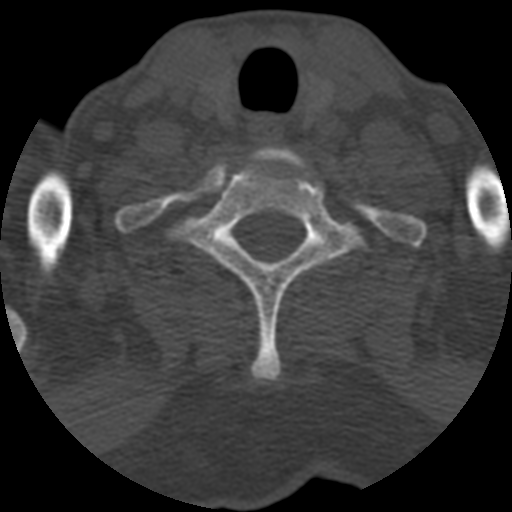
CT including the spine, one axial slice. Position 519 of 708 along the scan axis. Reconstruction kernel STANDARD. 120 kVp. One of 3 acquisitions stored at this slice position. Bone window (W 1800 / L 400 HU). 1.25 mm slice thickness. 512 × 512 image matrix. Patient age 55 years. From the clinical record (not read from this slice): primary cancer: colon; vertebrae with lytic lesions (as recorded): T12, L1, L5.
Annotated regions visible in this slice (semi-automatically segmented with operator editing):
- T1 vertebra: bounding box <169,152,362,382> (left, top, right, bottom; pixels)